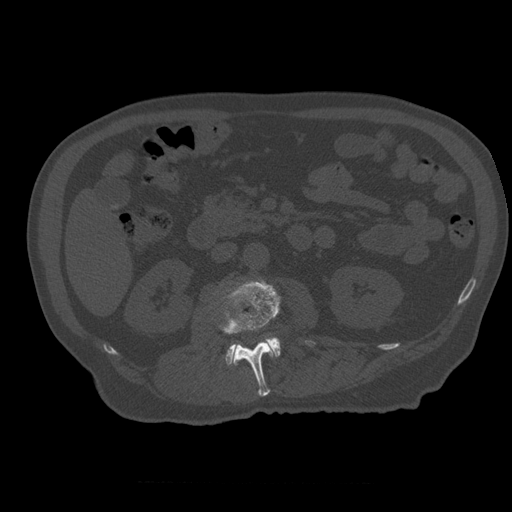
CT including the spine, one axial slice; position 207 of 399 along the scan axis; reconstruction kernel STANDARD; 120 kVp; bone window (W 1800 / L 400 HU); 1.25 mm slice thickness; 512 × 512 image matrix. Patient age 73 years. From the clinical record (not read from this slice): primary cancer: prostate.
Outlined on this slice (semi-automatically segmented with operator editing):
- L2 vertebra: bounding box [x1, y1, x2, y2] px = [219, 280, 280, 397]
- L3 vertebra: [226, 337, 281, 366]